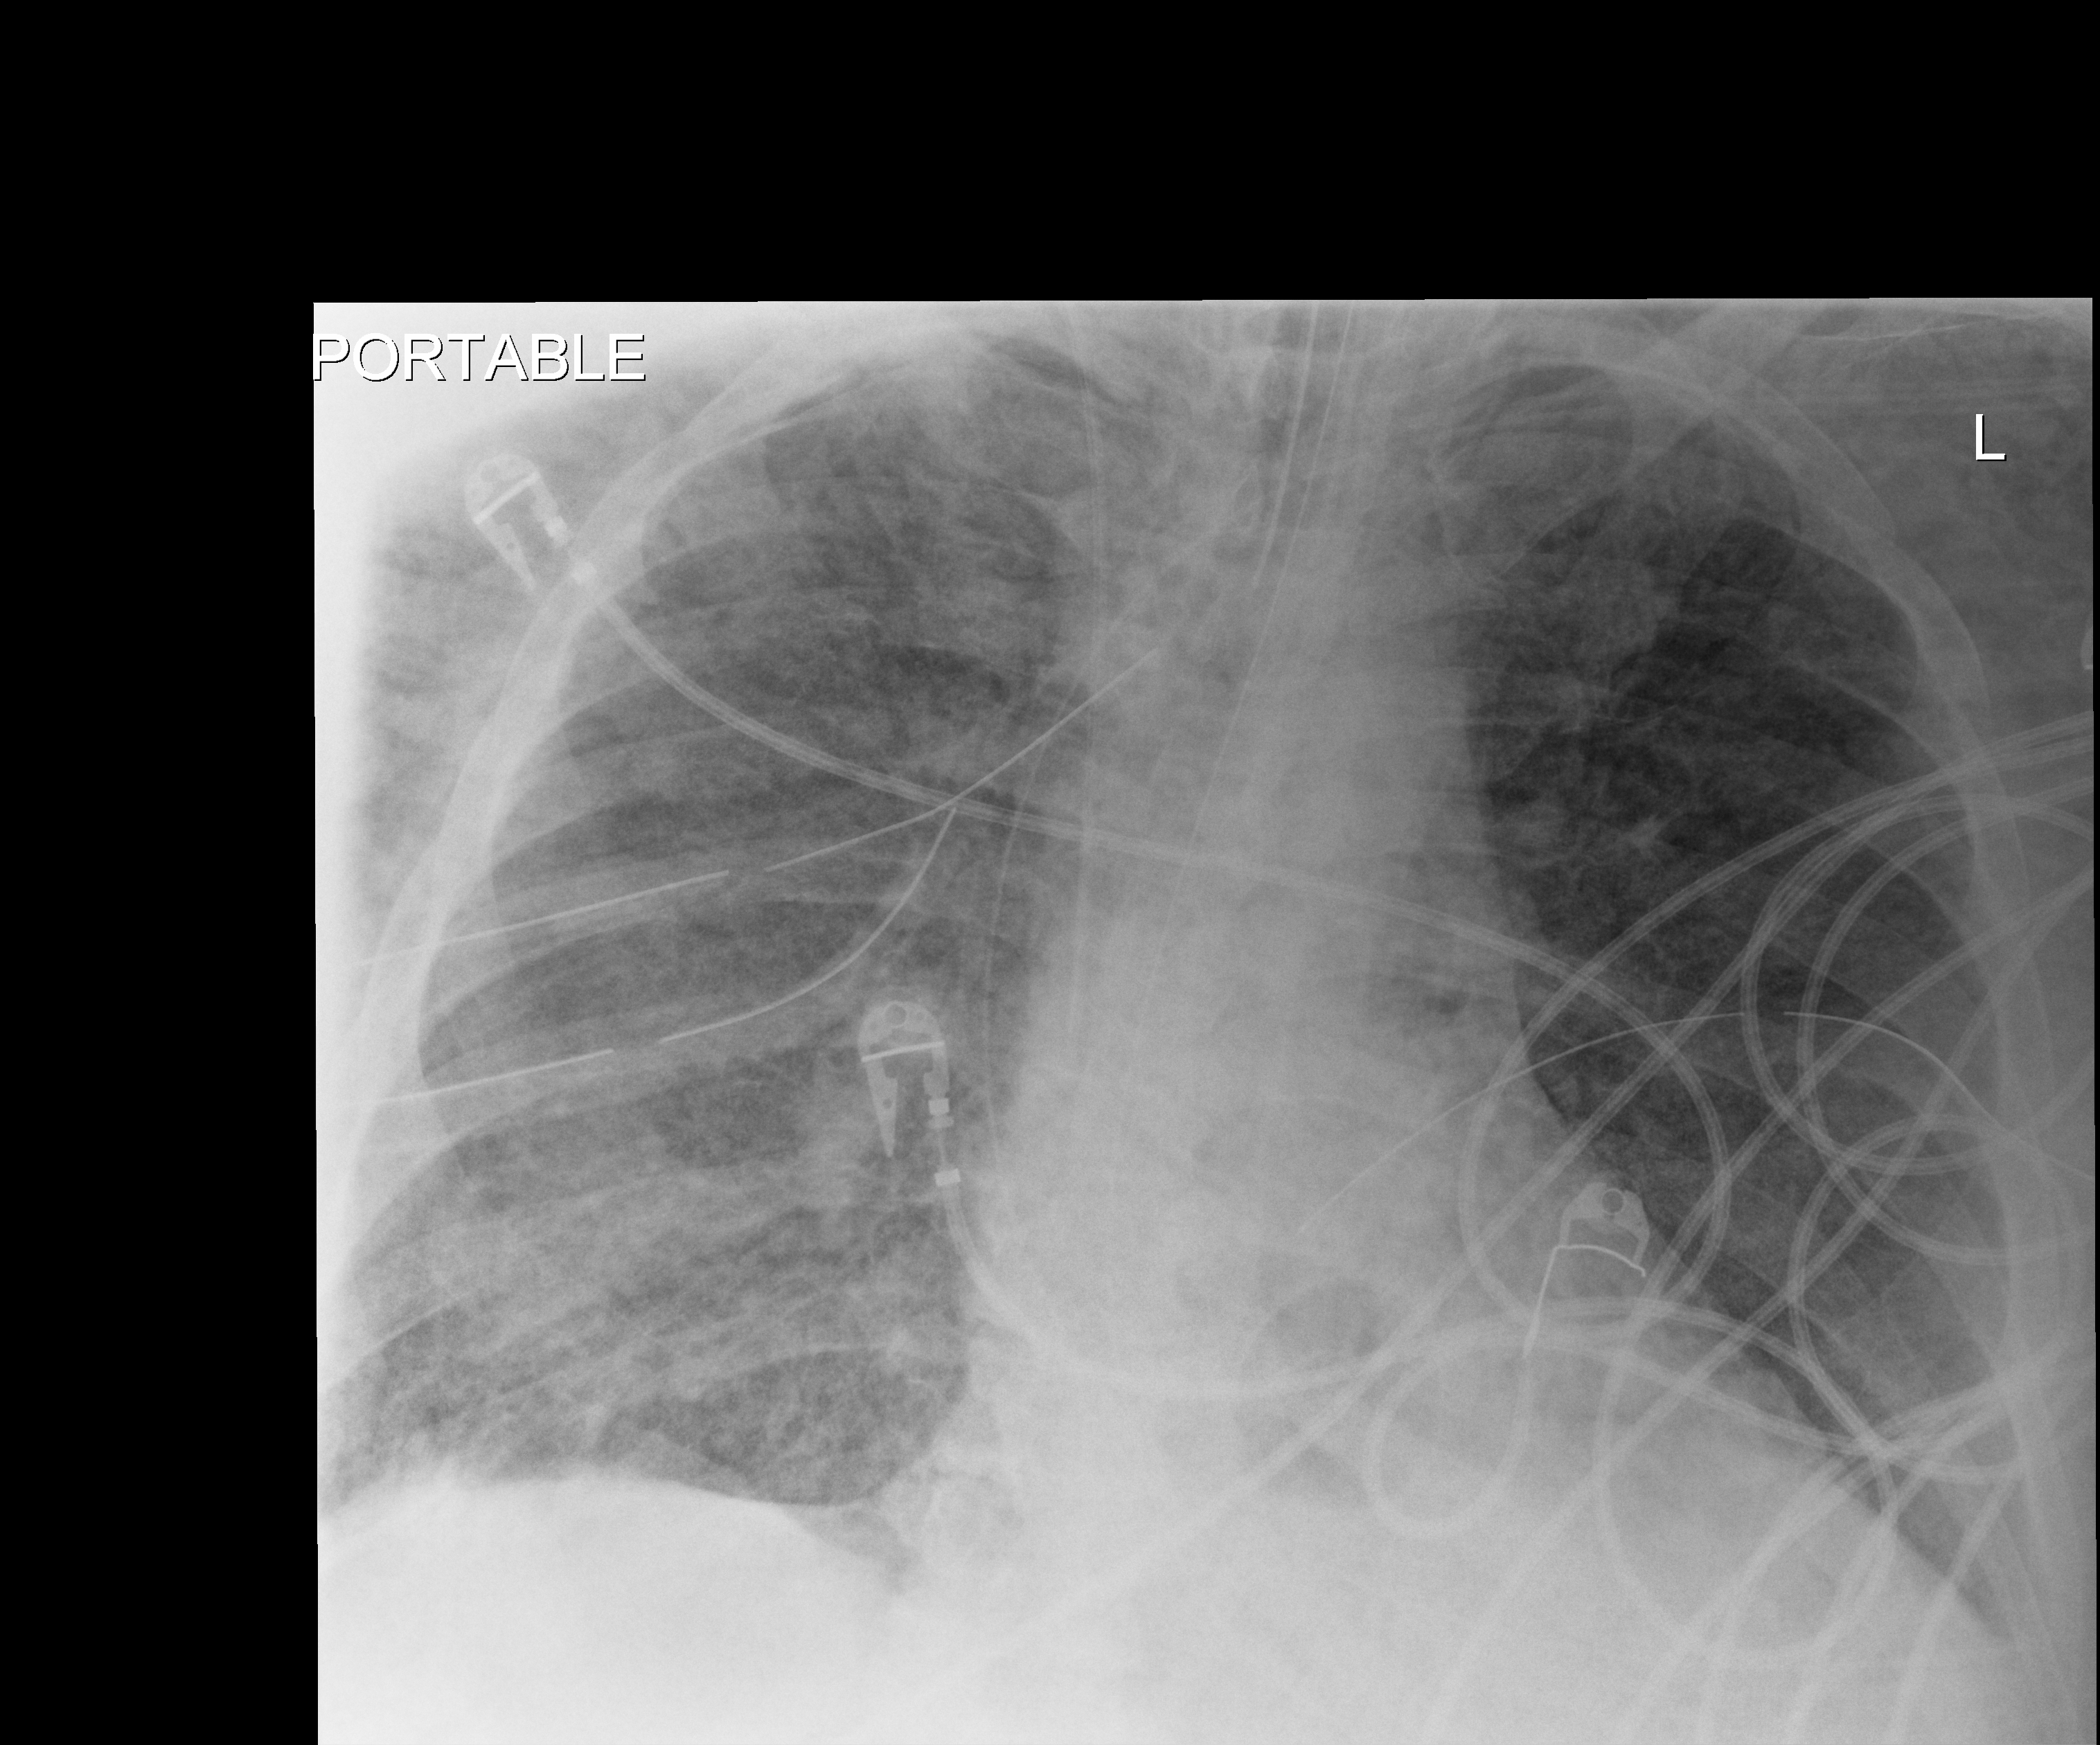
Chest X-ray (portable), anteroposterior (AP) projection. Adult patient hospitalised with COVID-19, age 18–59 years.
From the hospital-stay record, not from the radiograph (when in the stay this image was taken is not recorded): admitted to intensive care during this hospital stay: yes.